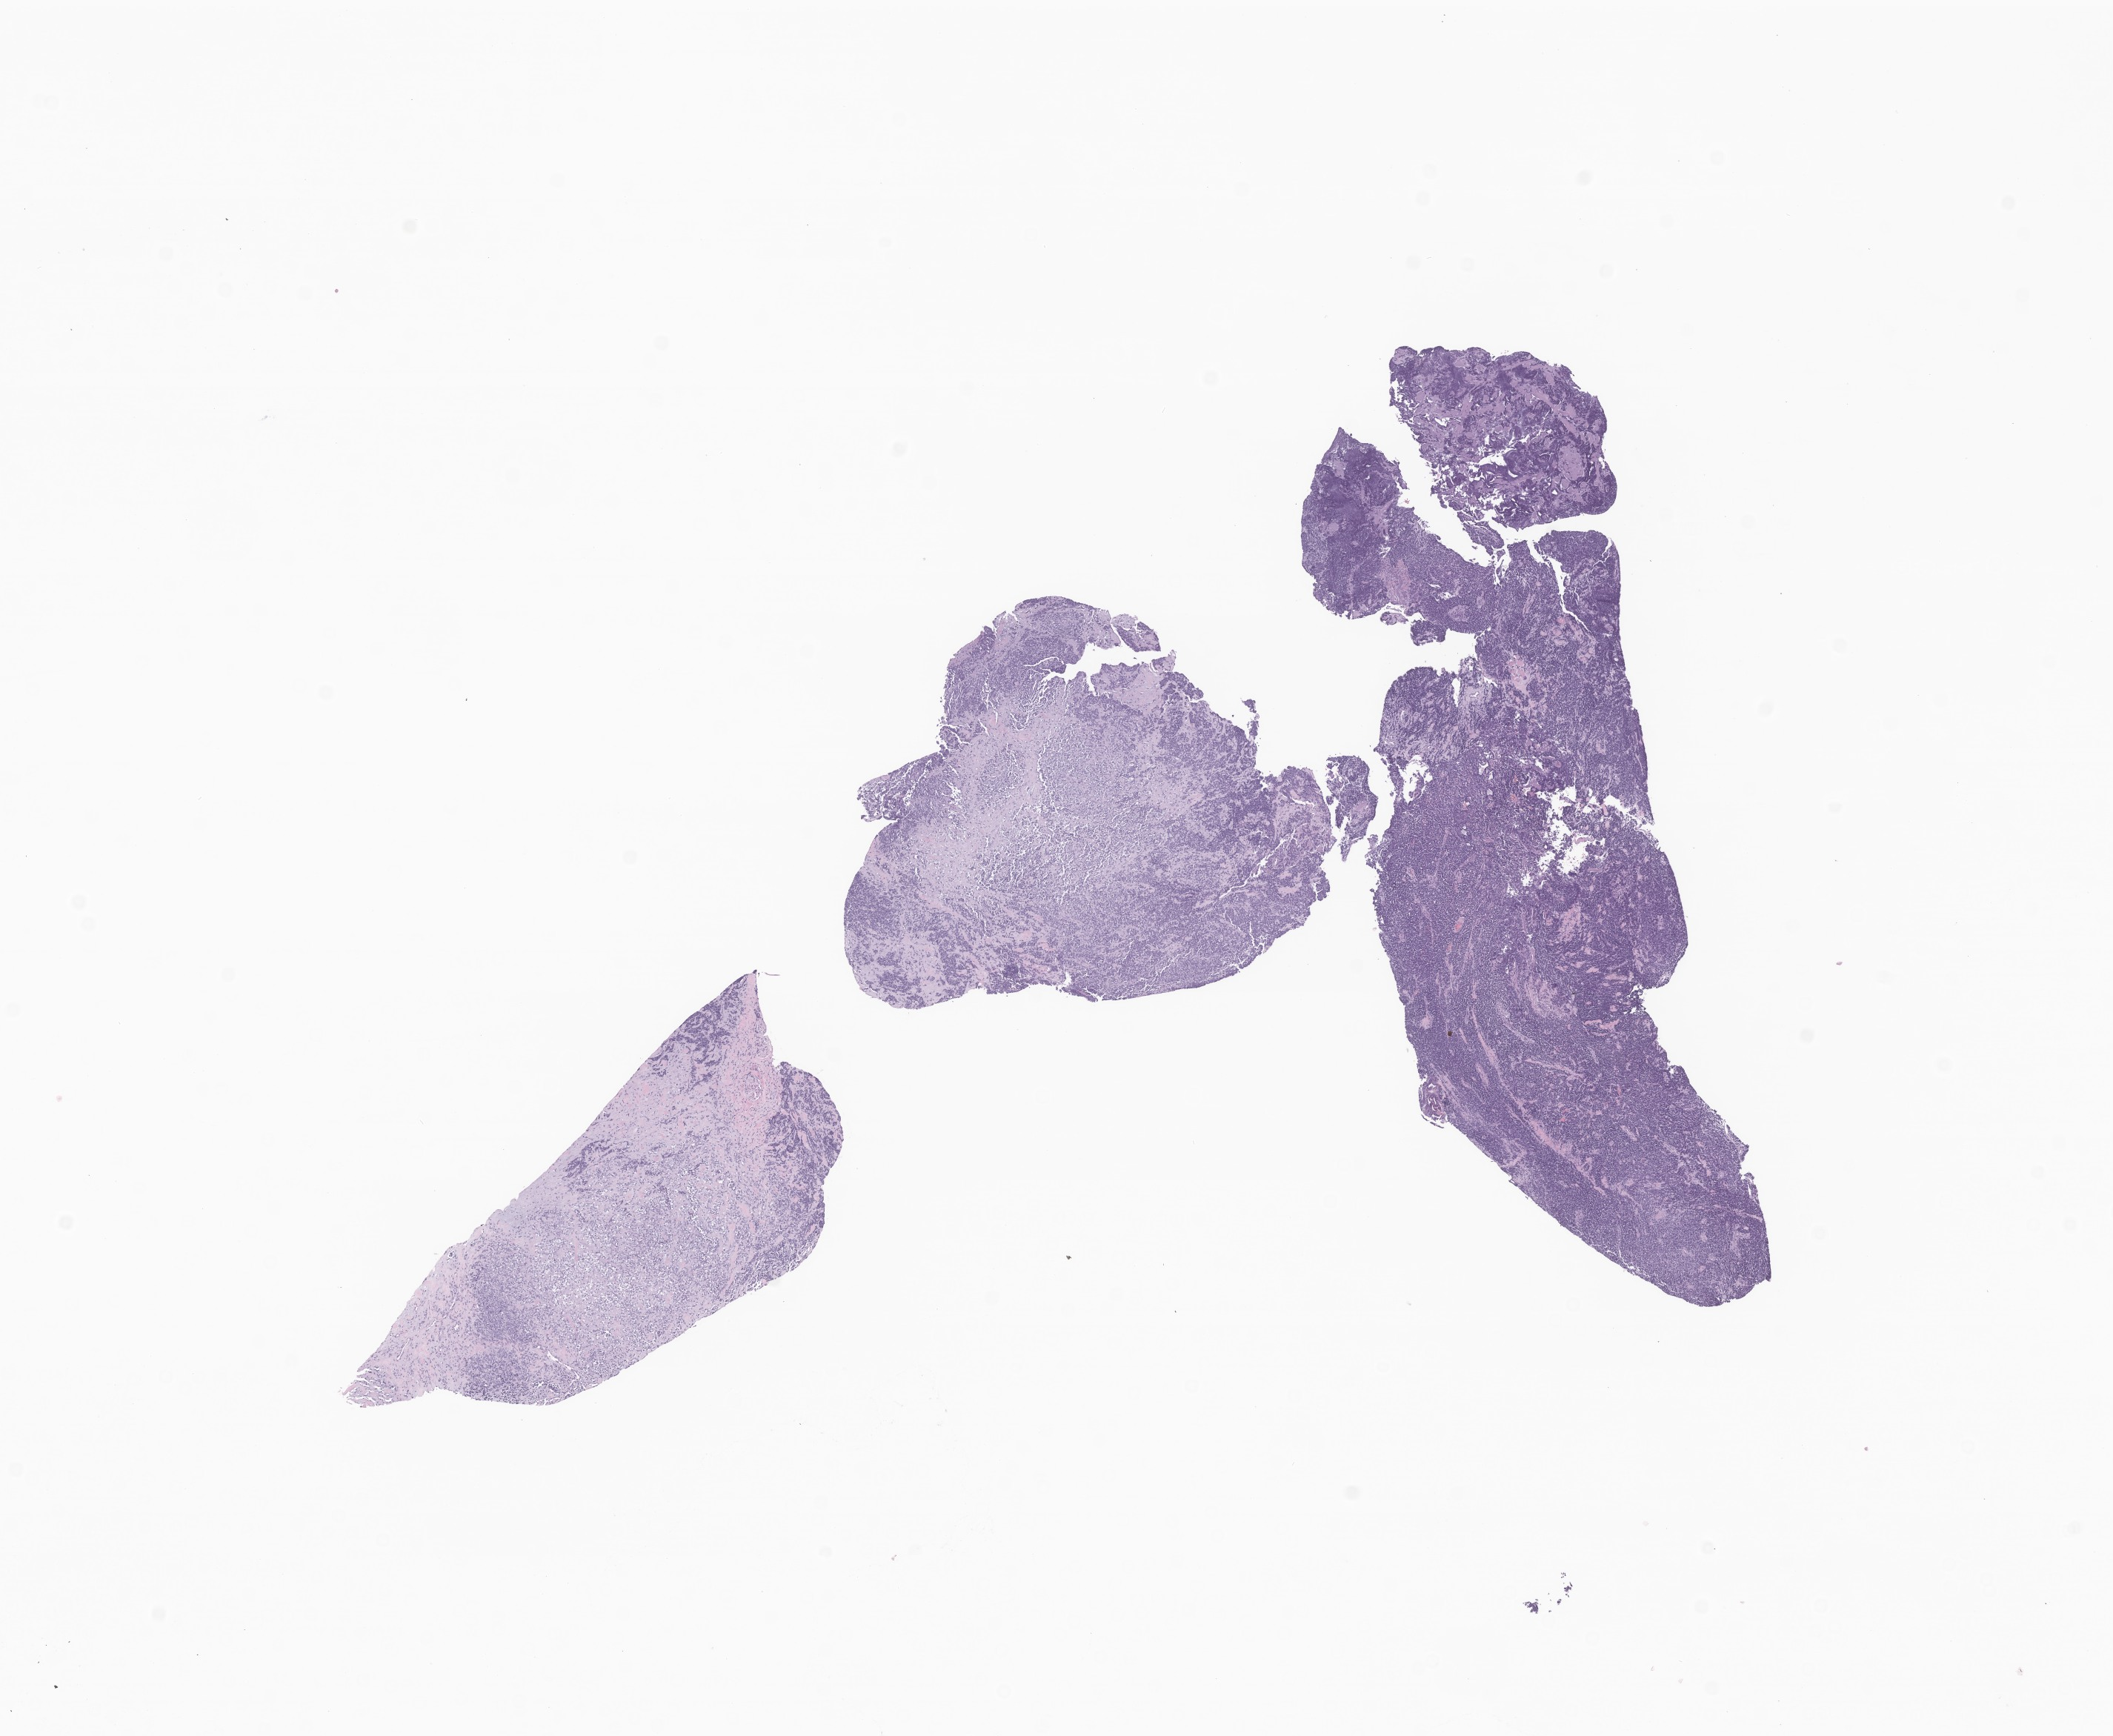
Digitized hematoxylin and eosin (H&E)-stained section of tumor tissue from the mucosa of lip, shown as a low-resolution overview of the whole scanned area (about 12.0 x 9.9 mm). Formalin-fixed, paraffin-embedded (FFPE) tissue. Patient male; age 514 days (about 1.4 years).
• diagnosis (ICD-O-3 morphology term): Alveolar rhabdomyosarcoma